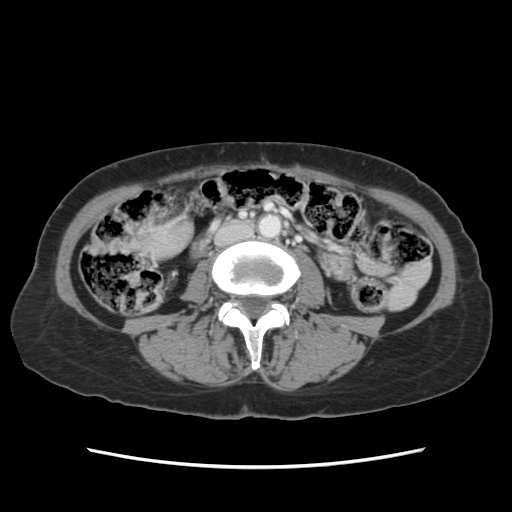
Contrast-enhanced abdominal CT, one axial slice. Slice 14 of 120 in the series (ordered by position). 120 kVp. Soft-tissue window (W 400 / L 40 HU). 2.5 mm slice thickness. 512 × 512 image matrix, field of view 330 × 330 mm. Female patient, age 70 years. From the clinical record (not read from this slice): diagnosis: colorectal cancer liver metastases, imaged before liver resection; multiple liver metastases: no; largest metastasis: 2.5 cm; disease in both lobes: no.
Structures marked on this image (expert manual segmentation):
- liver: bounding box (x1, y1, x2, y2) in pixels: (141, 224, 187, 252)
- planned liver remnant (the part of the liver to remain after resection): (141, 224, 187, 253)